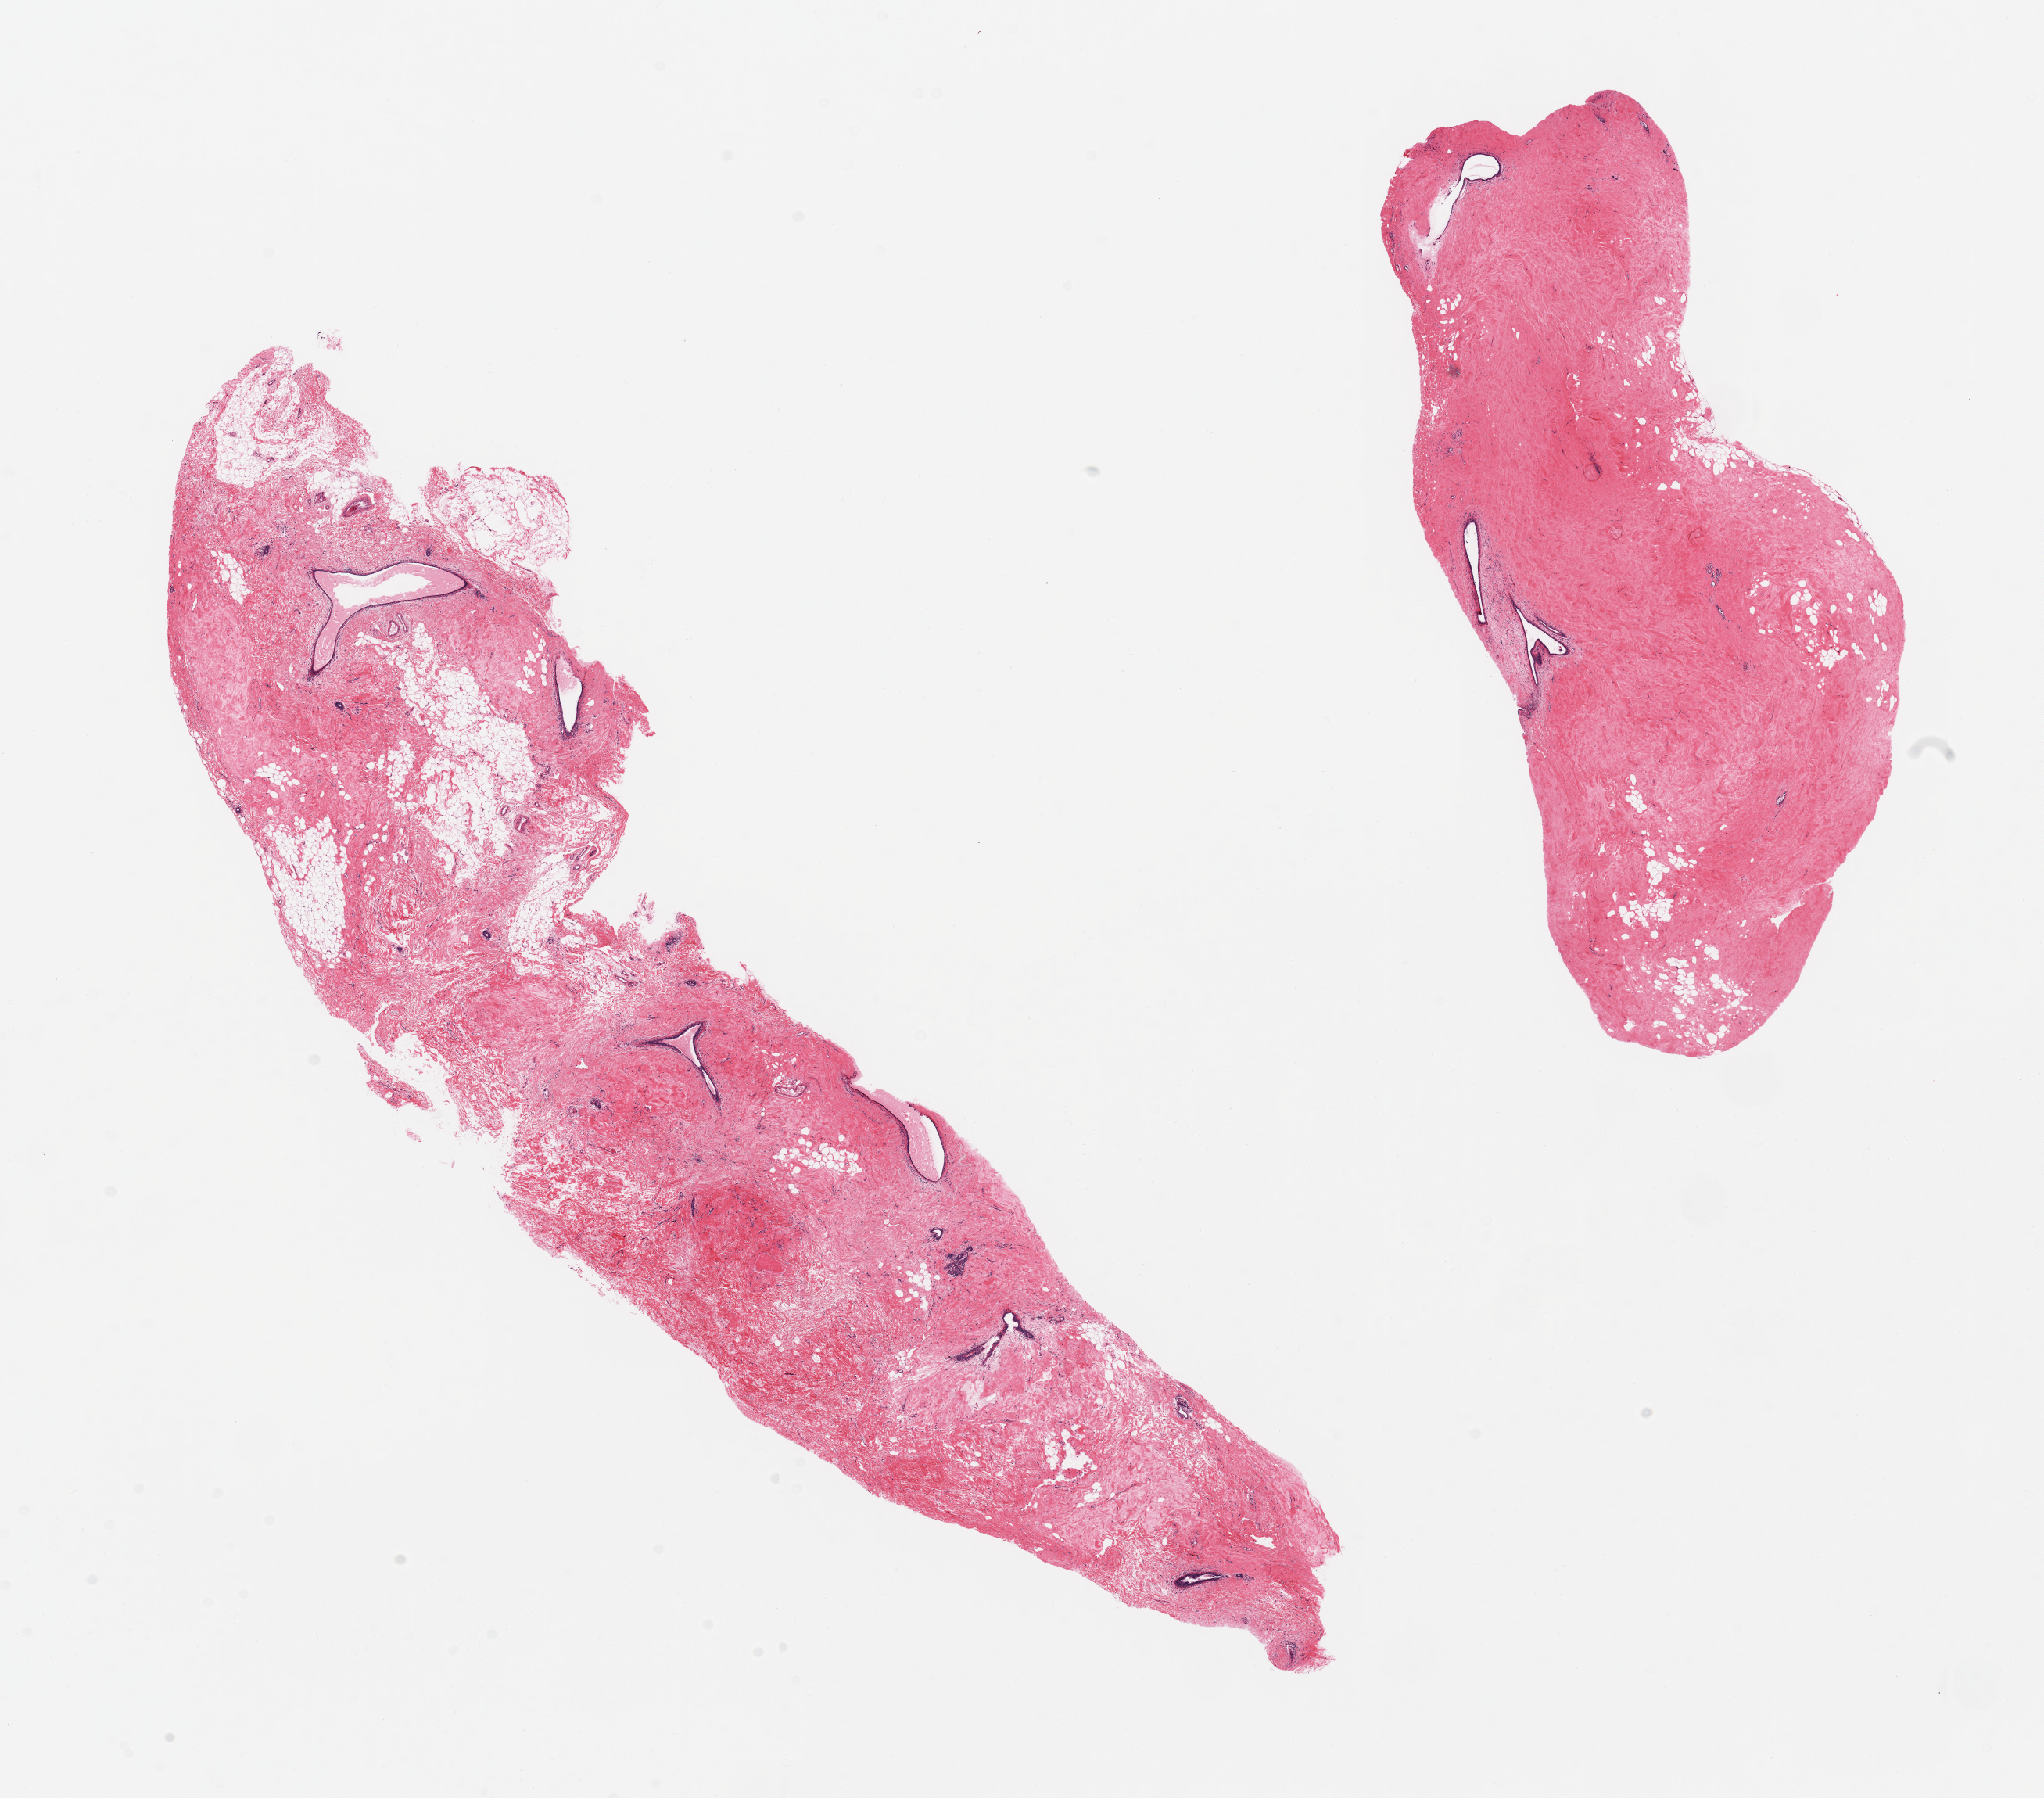
Whole-slide image, H&E stain, whole scanned area (about 20.7 x 18.2 mm, slide scanned at 20x) shown as a low-resolution overview; PAXgene-fixed, paraffin-embedded tissue; section of breast (target tissue); donor tissue sample. Donor sex: female.
* pathologist's review note for this sample: 2 pieces, mild fibrocystic change, rep ductal cysts